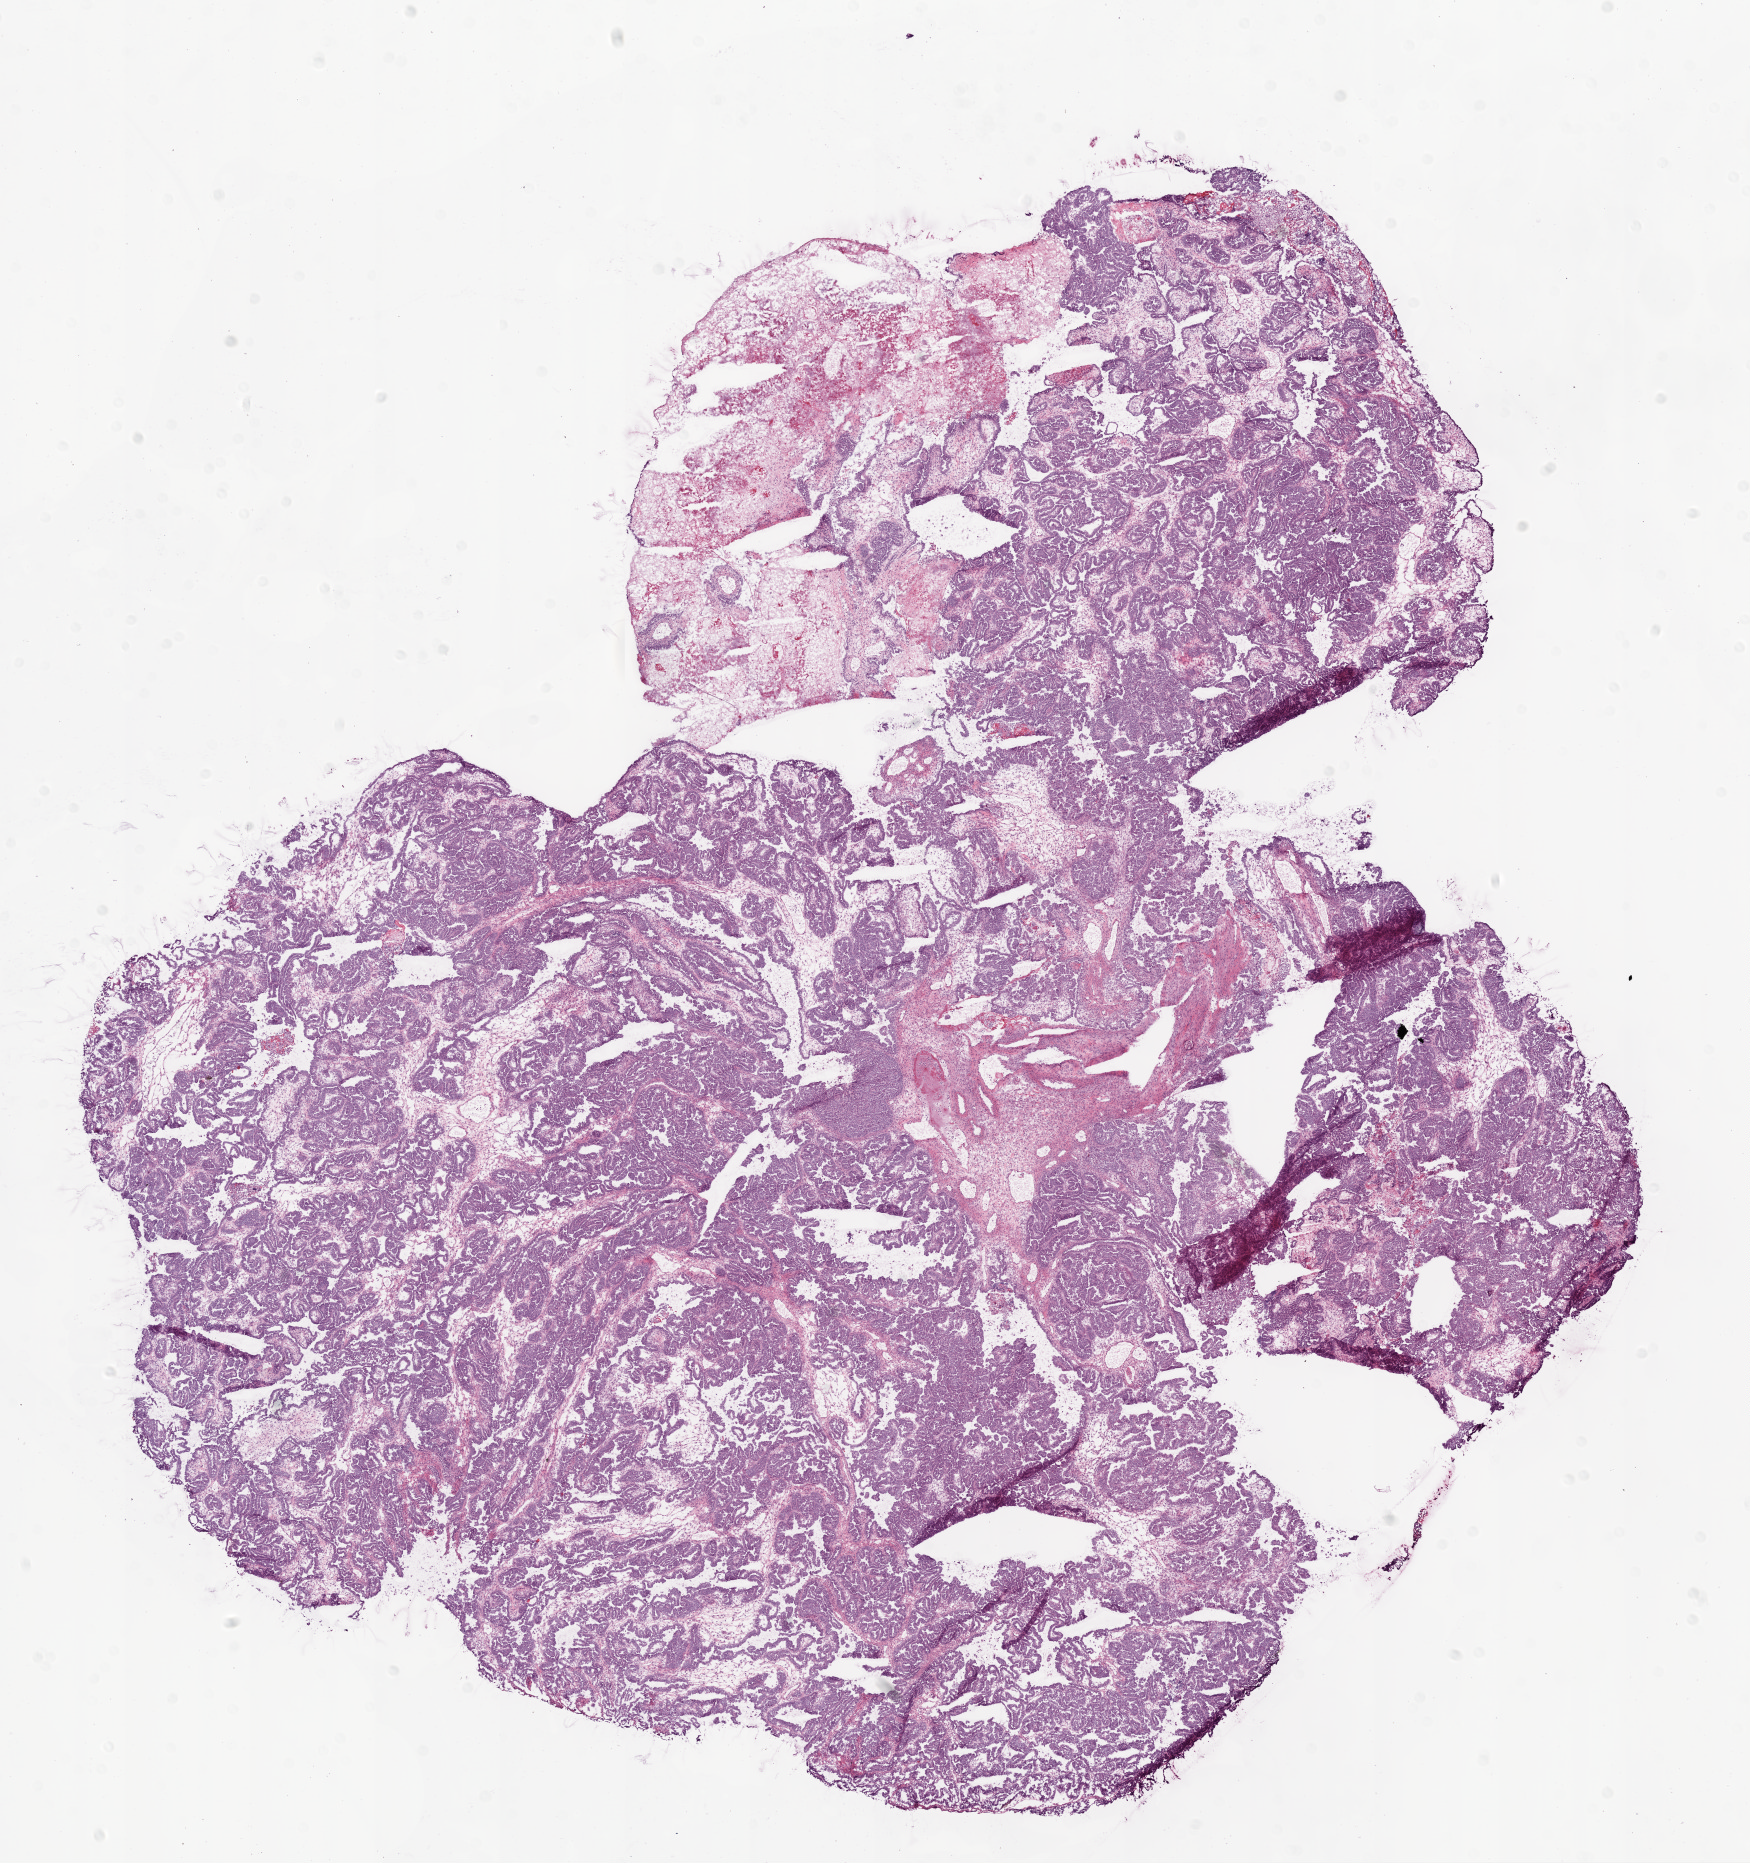
Digitized H&E tissue section (whole slide) — a low-resolution overview of the entire scanned area, about 14.0 x 14.9 mm; frozen section from the bottom of the tissue portion; primary tumour sample from the ovary. Female patient; age at initial diagnosis 59 years. Histologic grade: G2 (moderately differentiated). Slide review estimates, as recorded: tumour cells 85%, tumour nuclei 90%, normal cells 0%, stromal cells 5%, necrosis 10%.
Diagnosis: Serous cystadenocarcinoma, NOS. FIGO stage: IV. Laterality: bilateral.